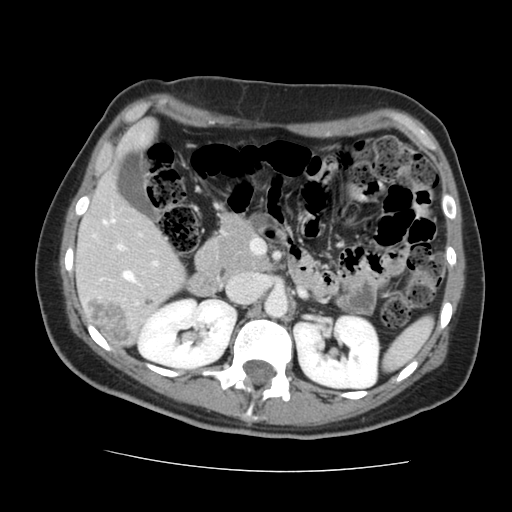
Contrast-enhanced abdominal CT, one axial slice. Position 78 of 144 along the scan axis. 120 kVp. Intravenous contrast given. Soft-tissue window (W 400 / L 40 HU). 2.5 mm slice thickness. 512 × 512 image matrix. Female patient, age 46 years. From the clinical record (not read from this slice): diagnosis: colorectal cancer liver metastases, imaged before liver resection; multiple liver metastases: no; largest metastasis: 2.8 cm; chemotherapy before resection: yes.
Outlined on this slice (expert manual segmentation):
- liver: bounding box [x1, y1, x2, y2] px = [78, 125, 185, 345]
- planned liver remnant (the part of the liver to remain after resection): [78, 125, 185, 335]
- portal vein (with intrahepatic branches): [103, 220, 156, 283]
- liver metastasis: [147, 301, 153, 306]
- liver metastasis: [89, 300, 133, 343]